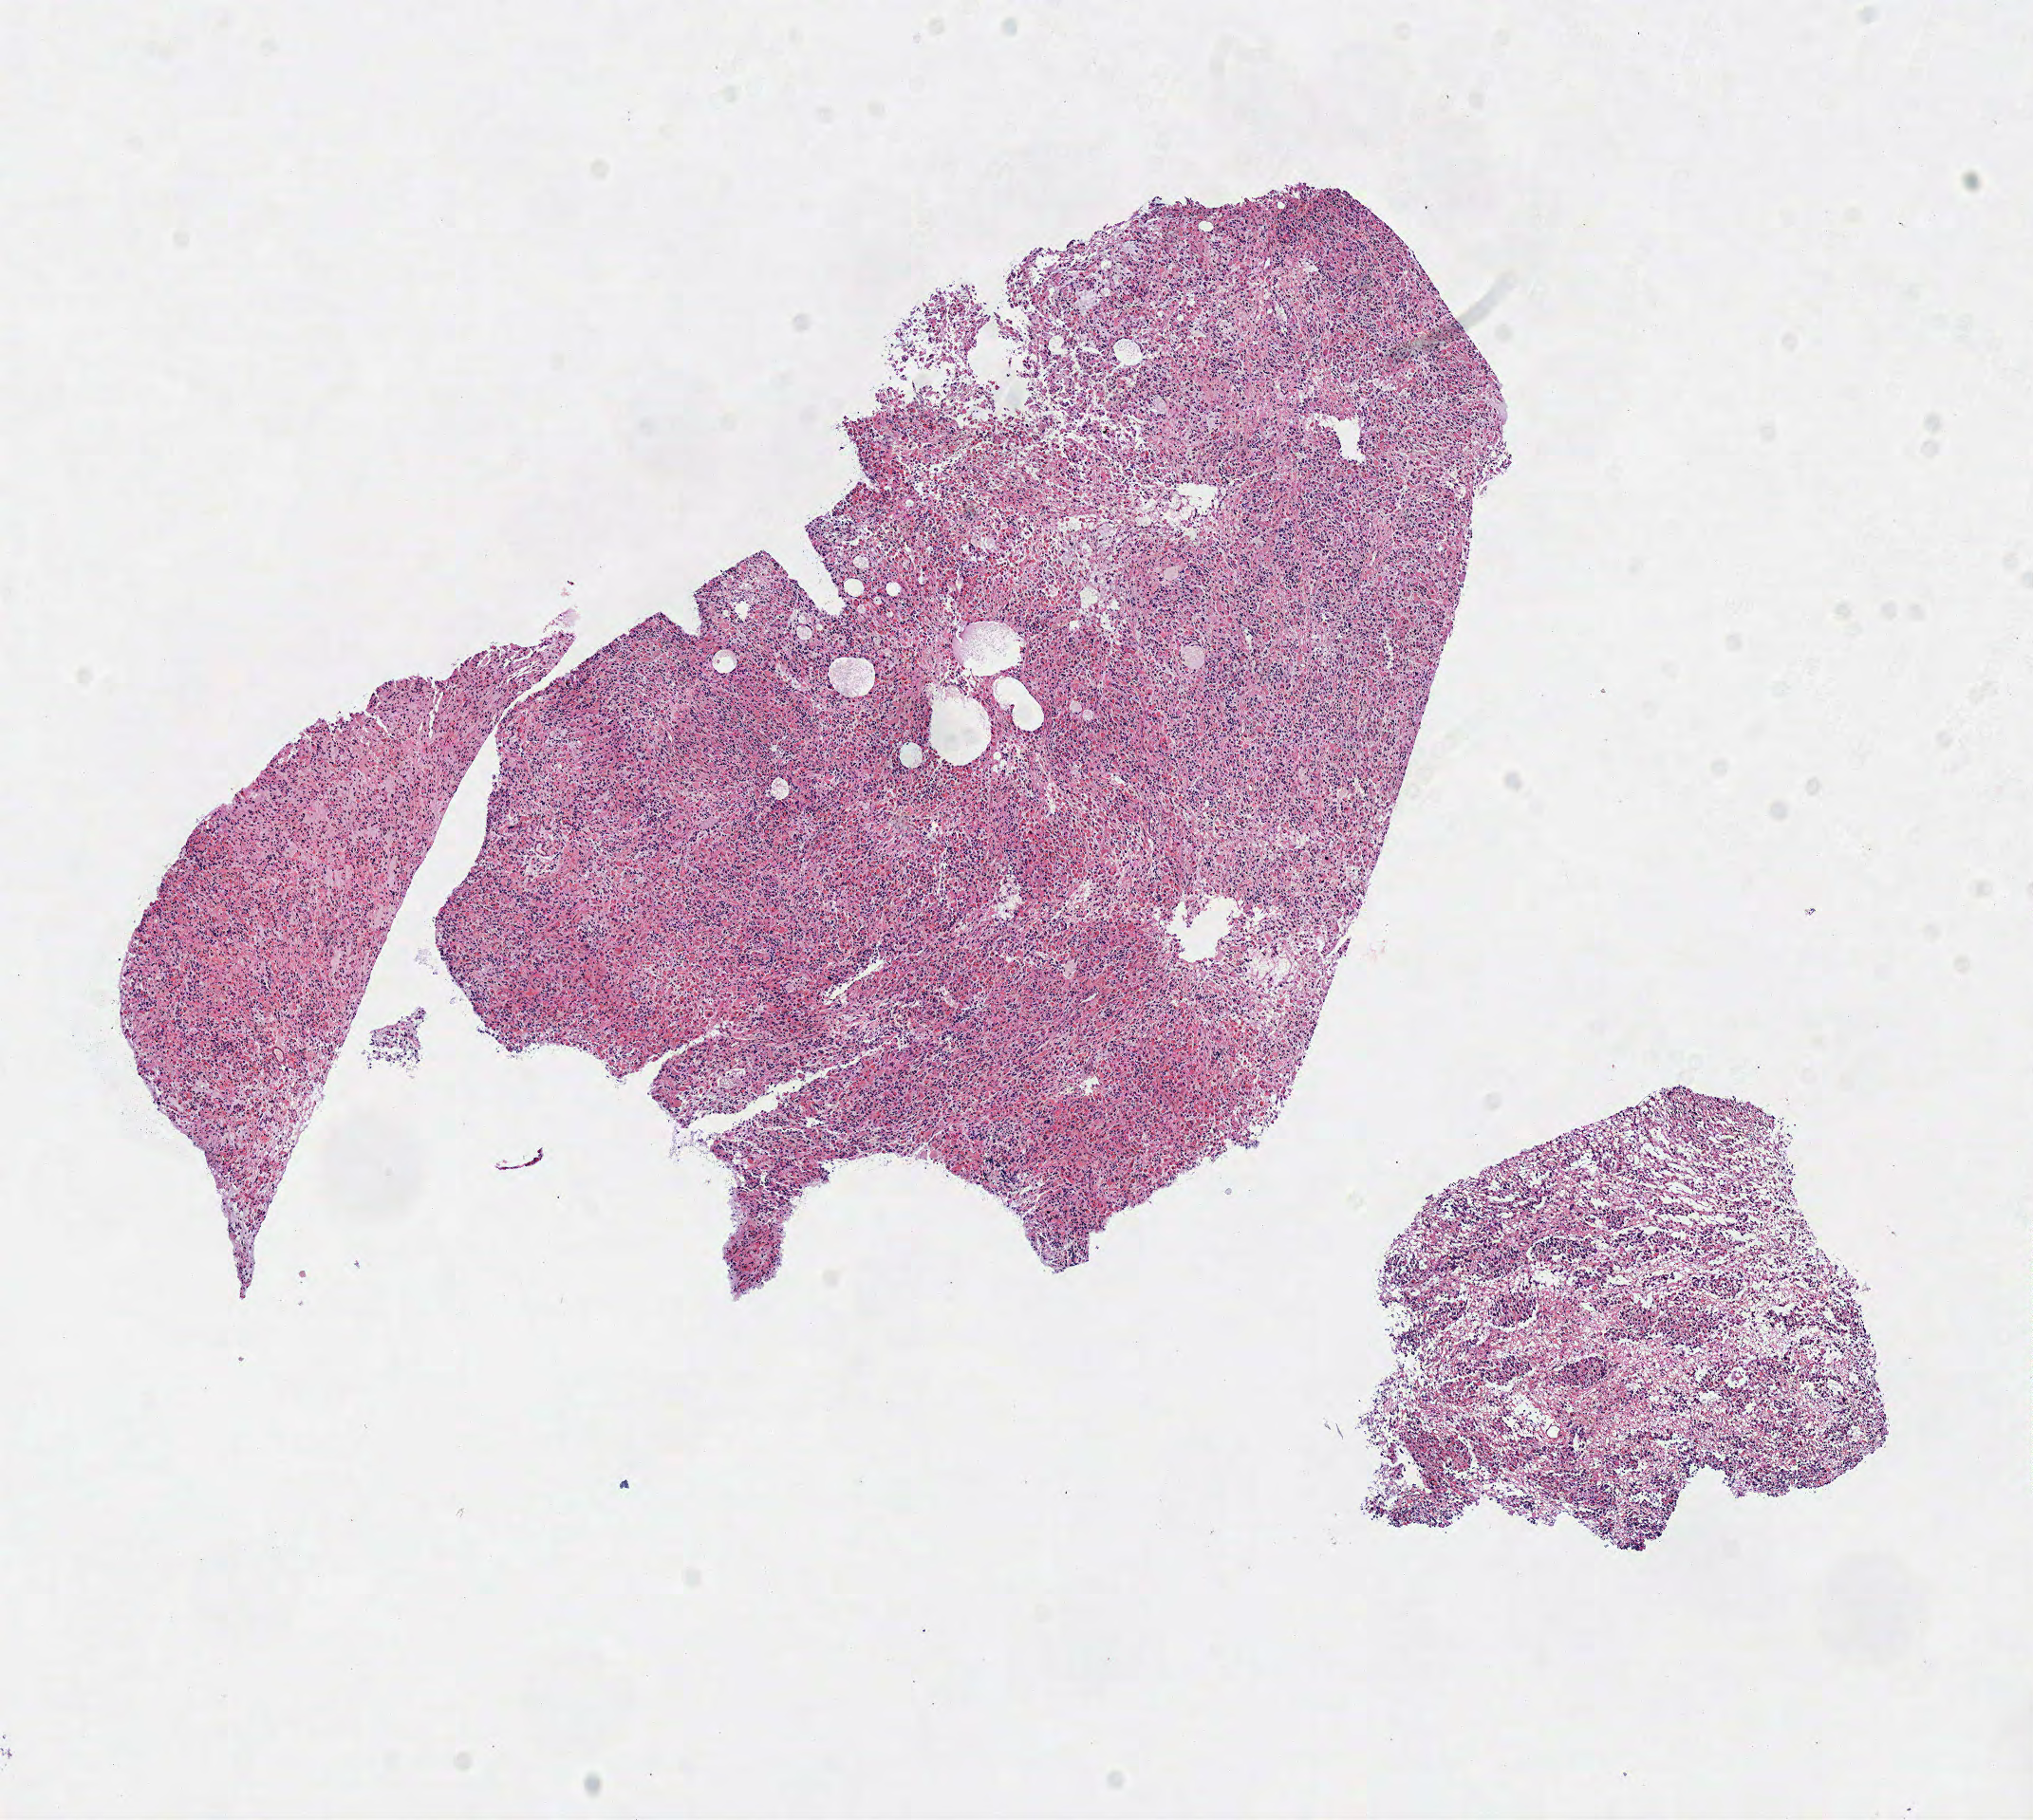
H&E whole-slide image, low-resolution overview of the scanned area, about 8.4 x 7.6 mm (acquisition: 40x scan), frozen section from the top of the tissue portion, brain, primary tumour sample. Female patient; age at initial diagnosis 49 years. Histologic grade: G3 (poorly differentiated). Slide review estimates, as recorded: tumour cells 100%, tumour nuclei 80%, normal cells 0%, stromal cells 0%, necrosis 0%.
Histologic diagnosis: Mixed glioma. Laterality: right.